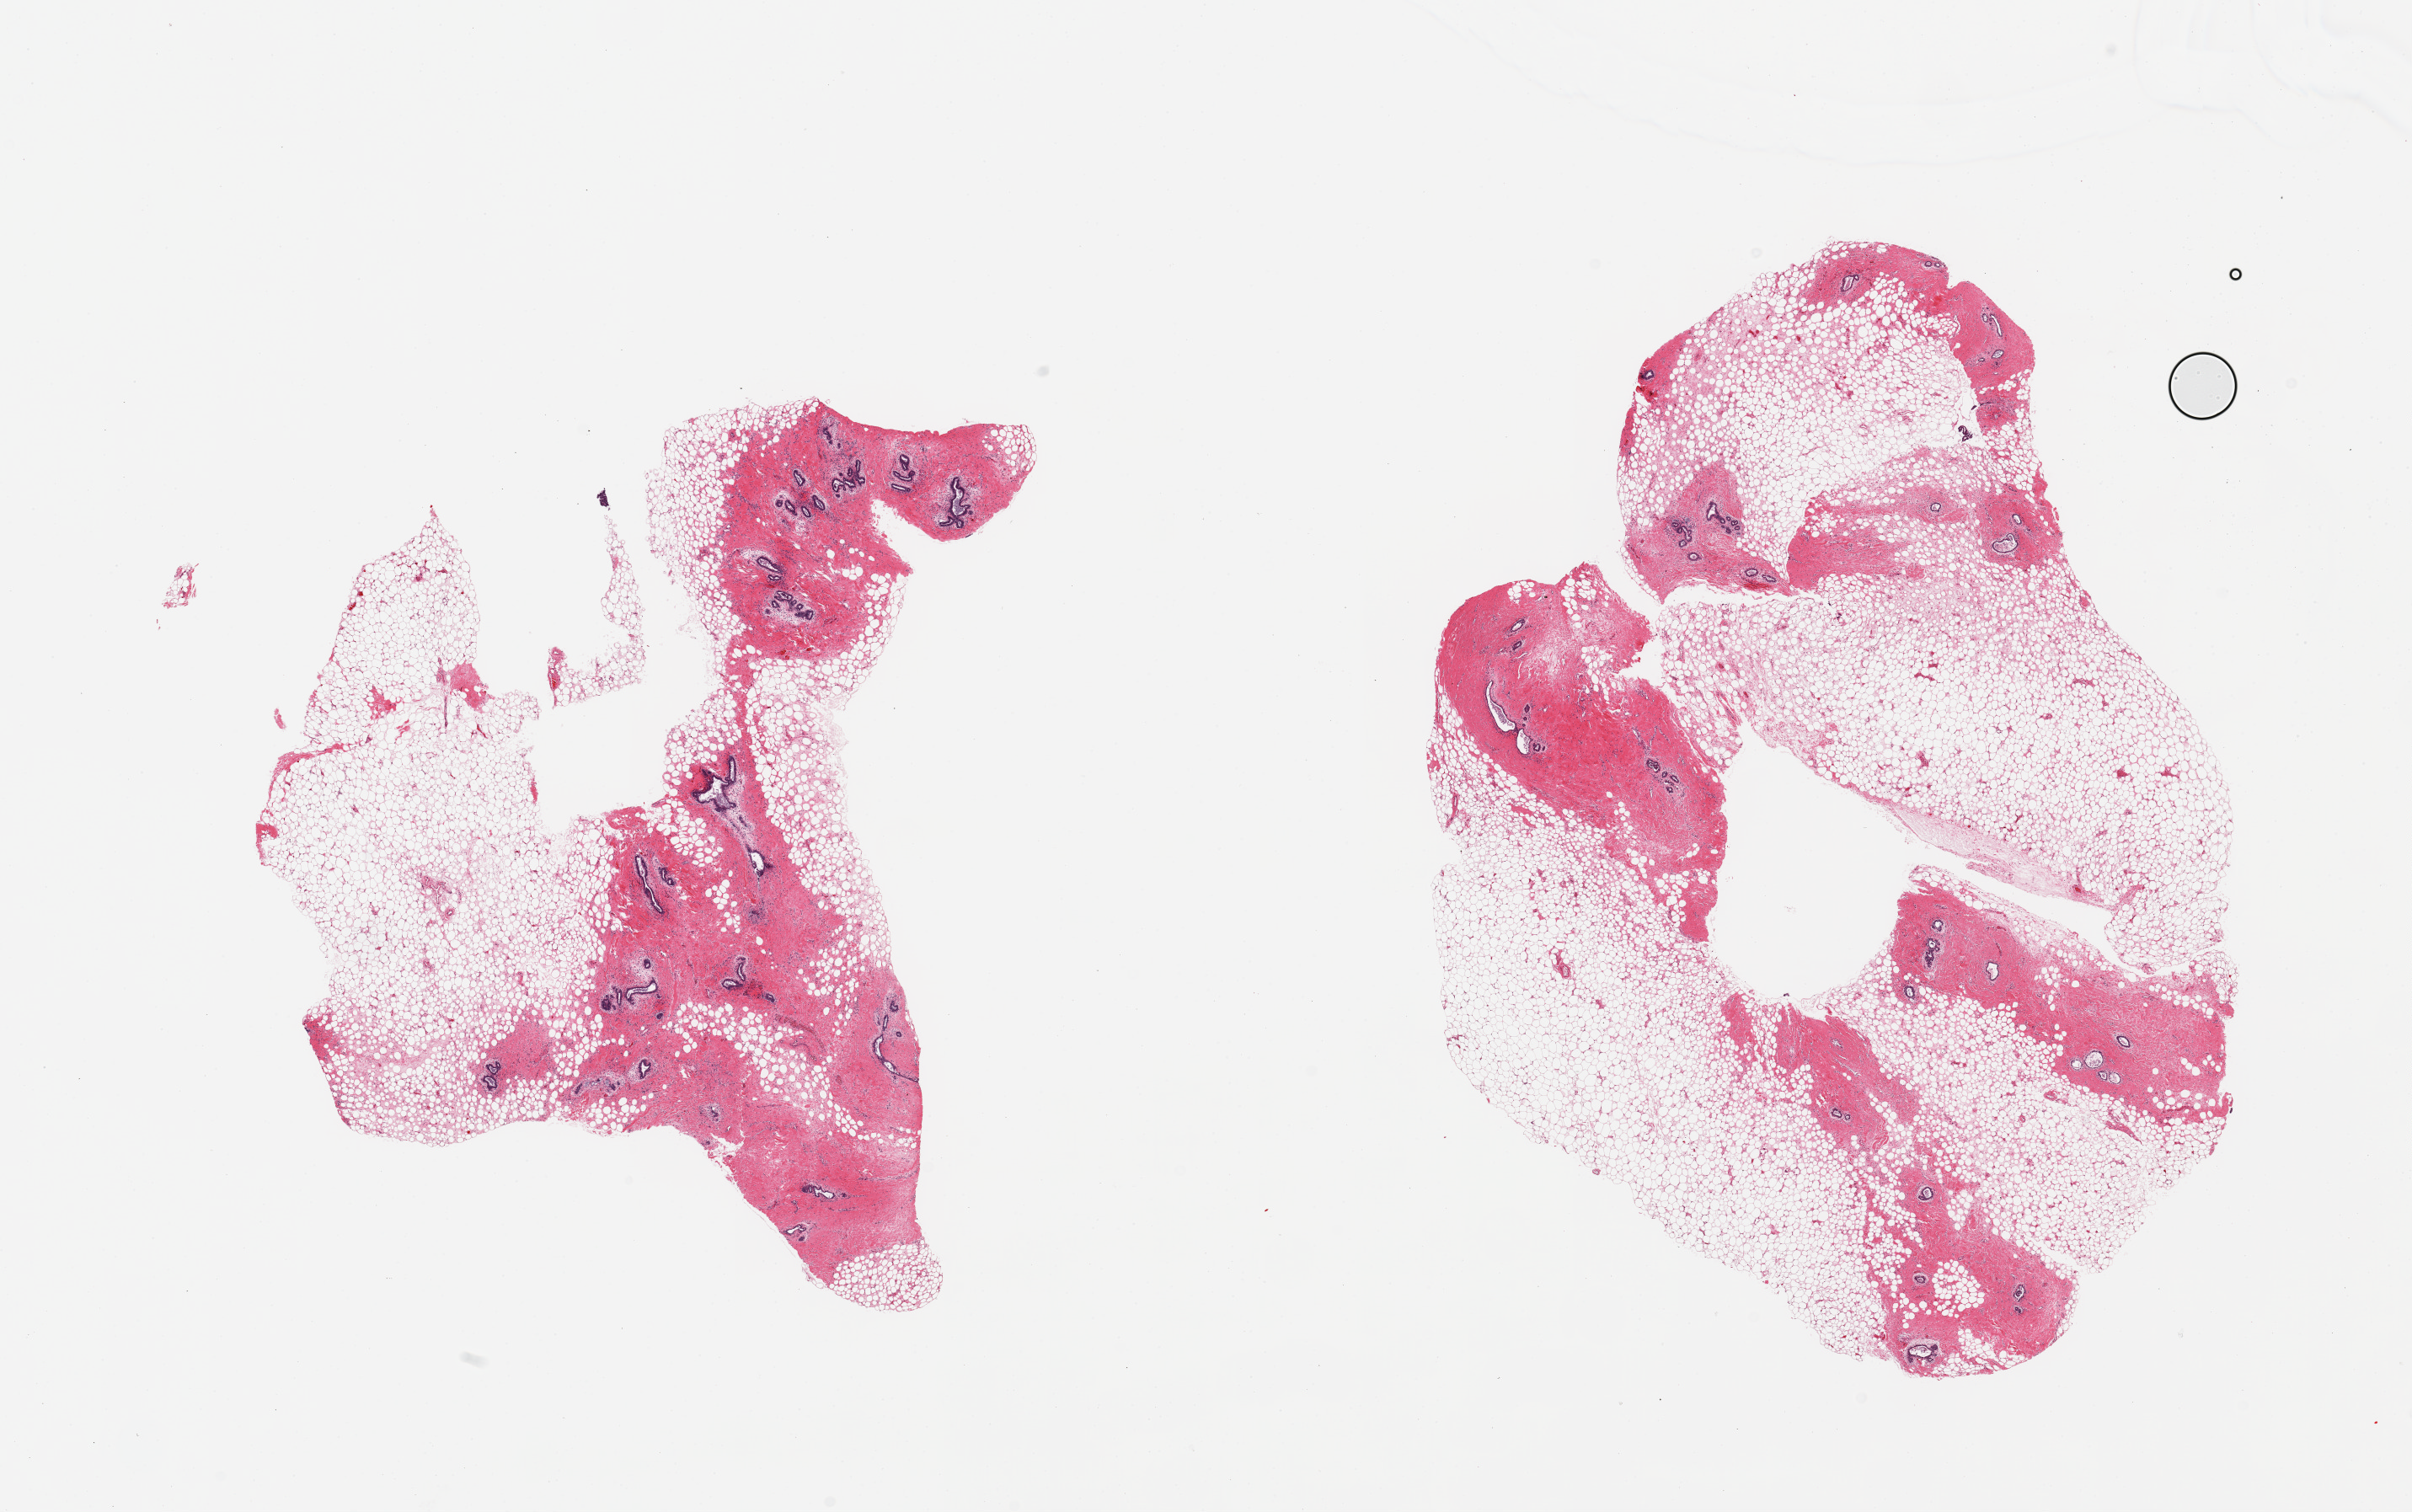
Whole-slide image, hematoxylin and eosin (H&E) stain — a low-resolution overview of the entire scanned area, about 22.6 x 14.2 mm; PAXgene-fixed, paraffin-embedded tissue; sampled site (target tissue): breast; tissue donor sample. Donor sex: male.
Pathologist's review note for this sample: 2 pieces, gynecomastoid hyperplasia, prominent ducts, focal PASH (pseudoangiomatoid stromal hyperplasia).